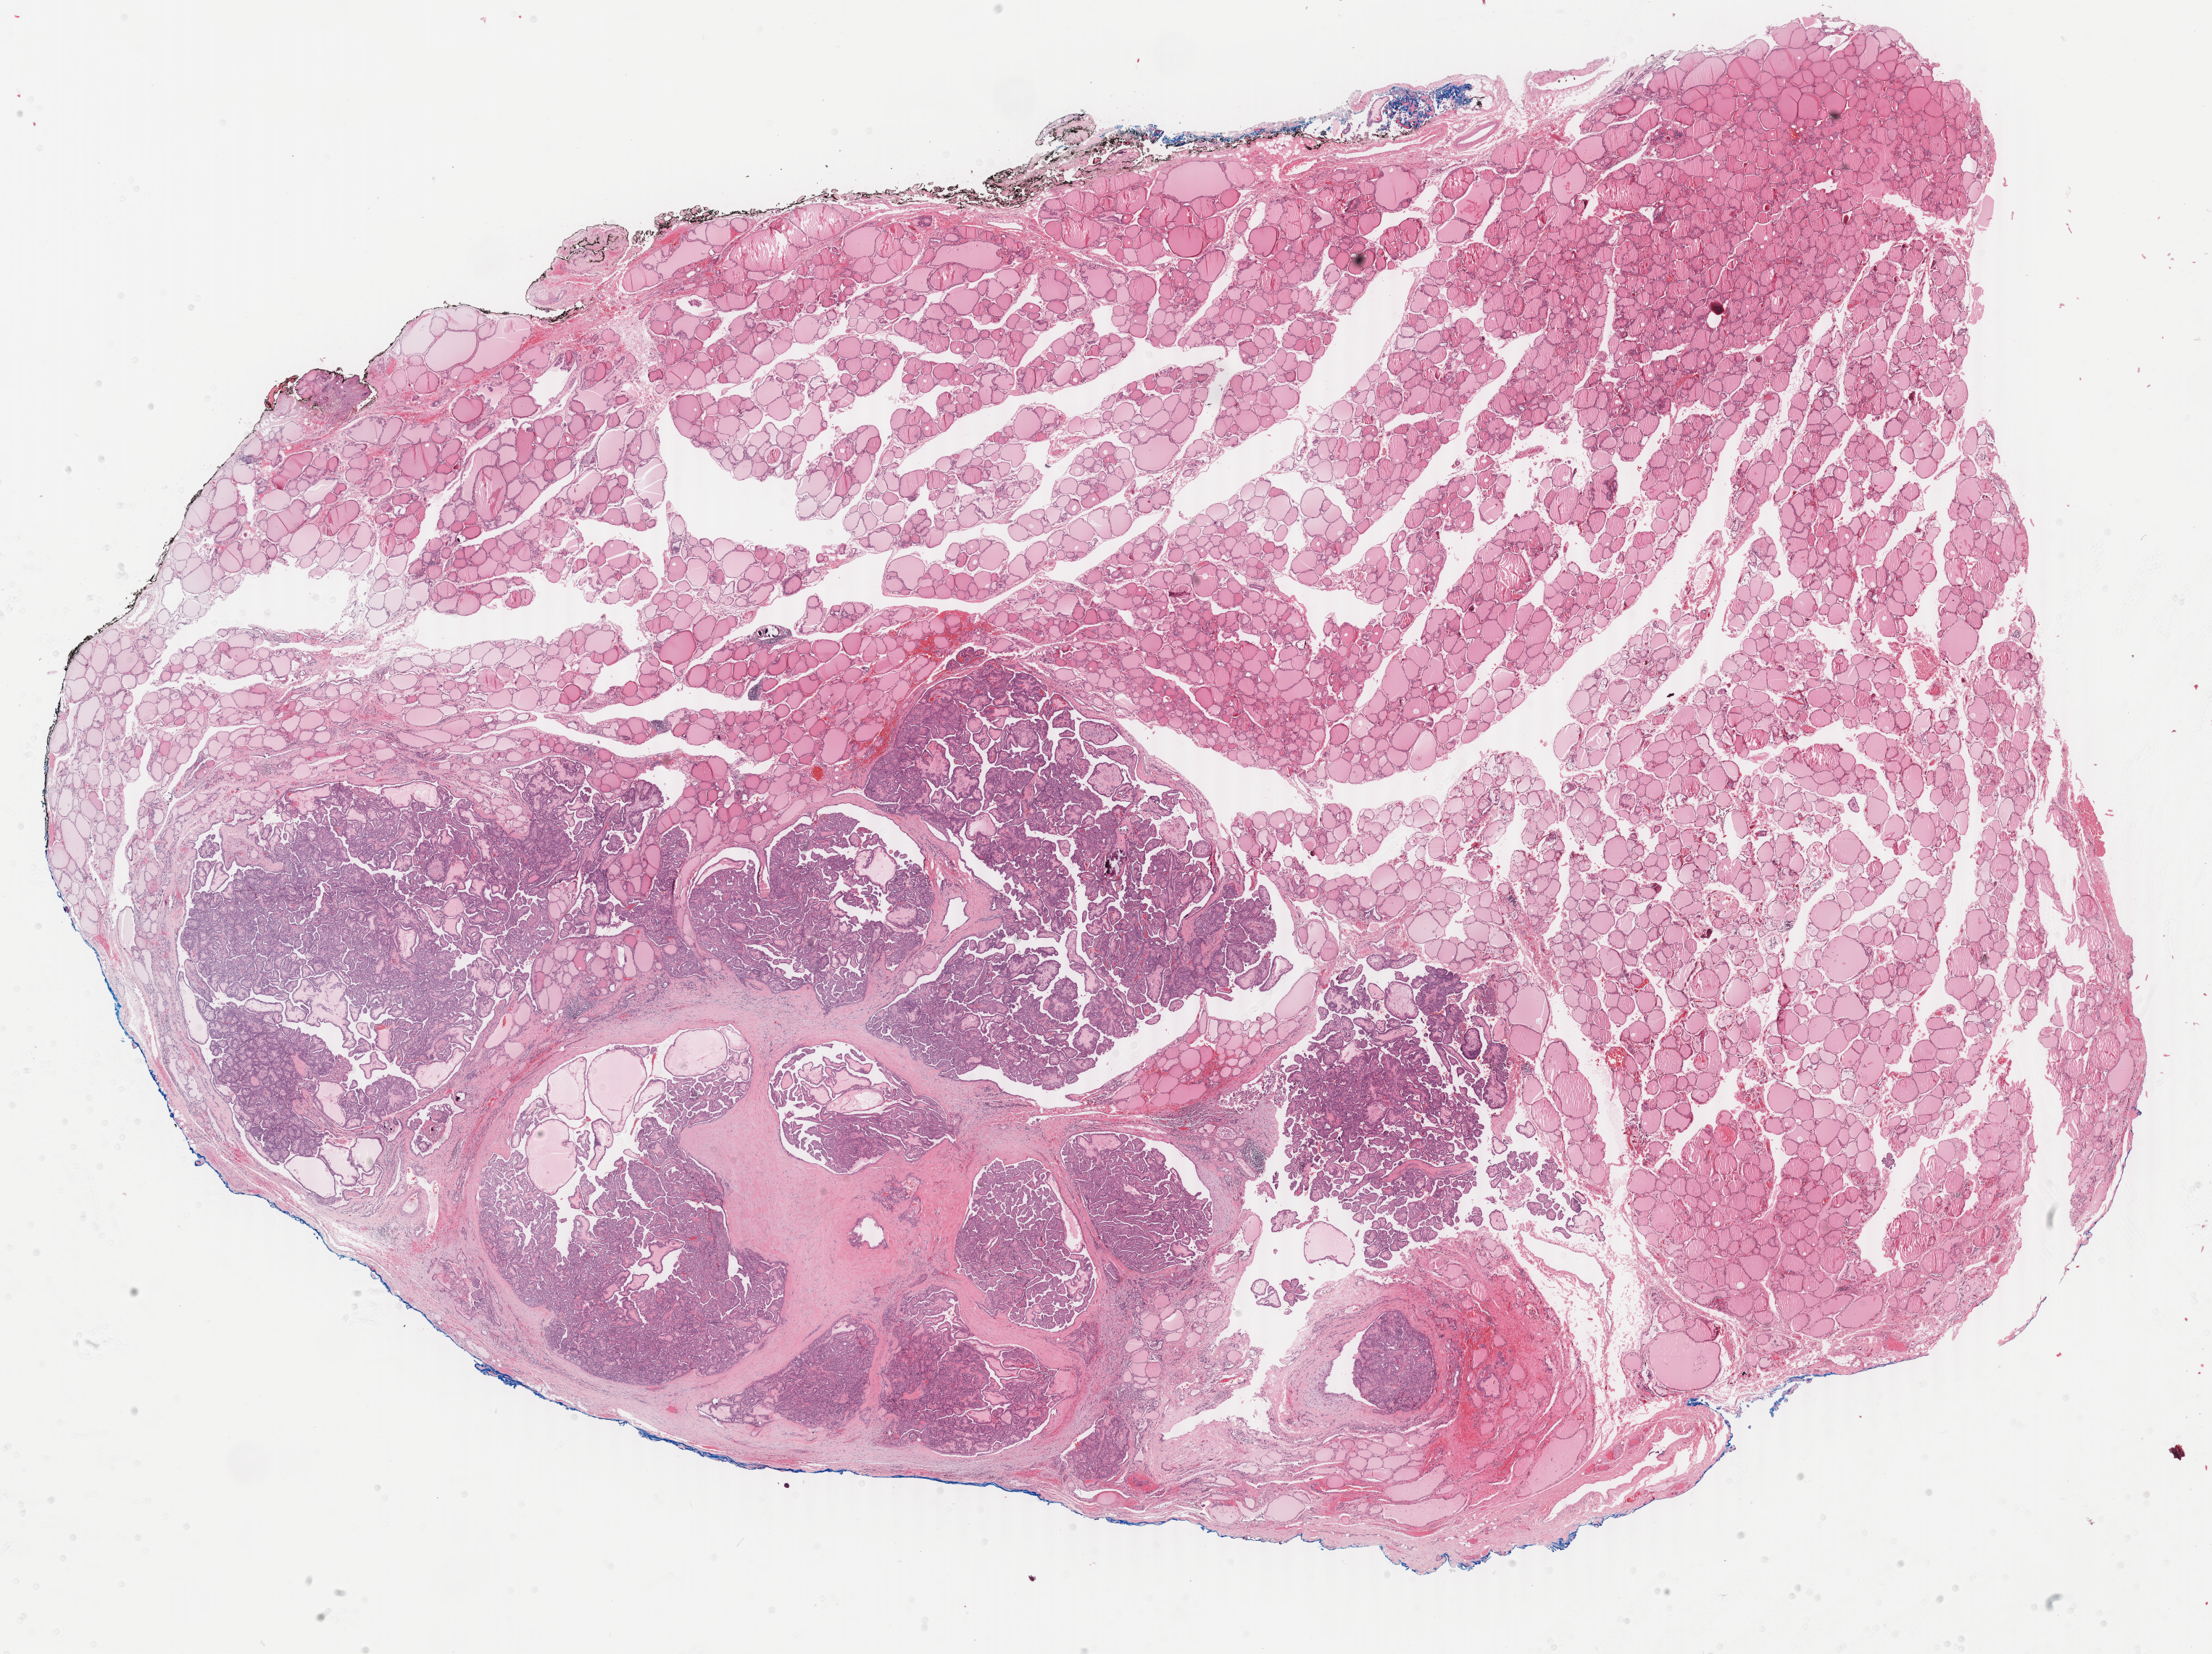
Whole-slide histology image, H&E, whole scanned area (about 24.3 x 18.1 mm, acquisition: 40x scan) shown as a low-resolution overview; formalin-fixed paraffin-embedded (FFPE) diagnostic section; primary tumour sample from the thyroid. Female patient; age at initial diagnosis 18 years.
Pathologic diagnosis: Papillary adenocarcinoma, NOS. AJCC pathologic stage: I (6th edition).